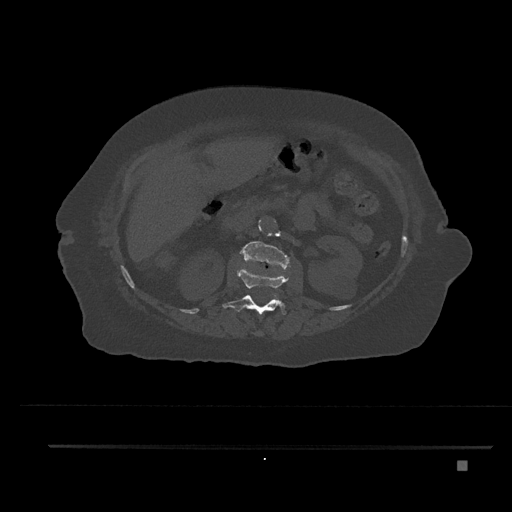
CT including the spine, one axial slice. Position 212 of 797 along the scan axis. Bone window (W 1800 / L 400 HU). 0.5 mm slice thickness. 512 × 512 image matrix. Patient: female, 76 years. Case-level facts recorded for this patient, not image findings: primary cancer: lung; vertebrae with lytic lesions (as recorded): T11, L3.
Annotated regions visible in this slice (semi-automatic segmentation, software-assisted and operator-edited):
- L1 vertebra: bounding box <222,268,297,317> (left, top, right, bottom; pixels)
- L2 vertebra: <240,241,290,274>